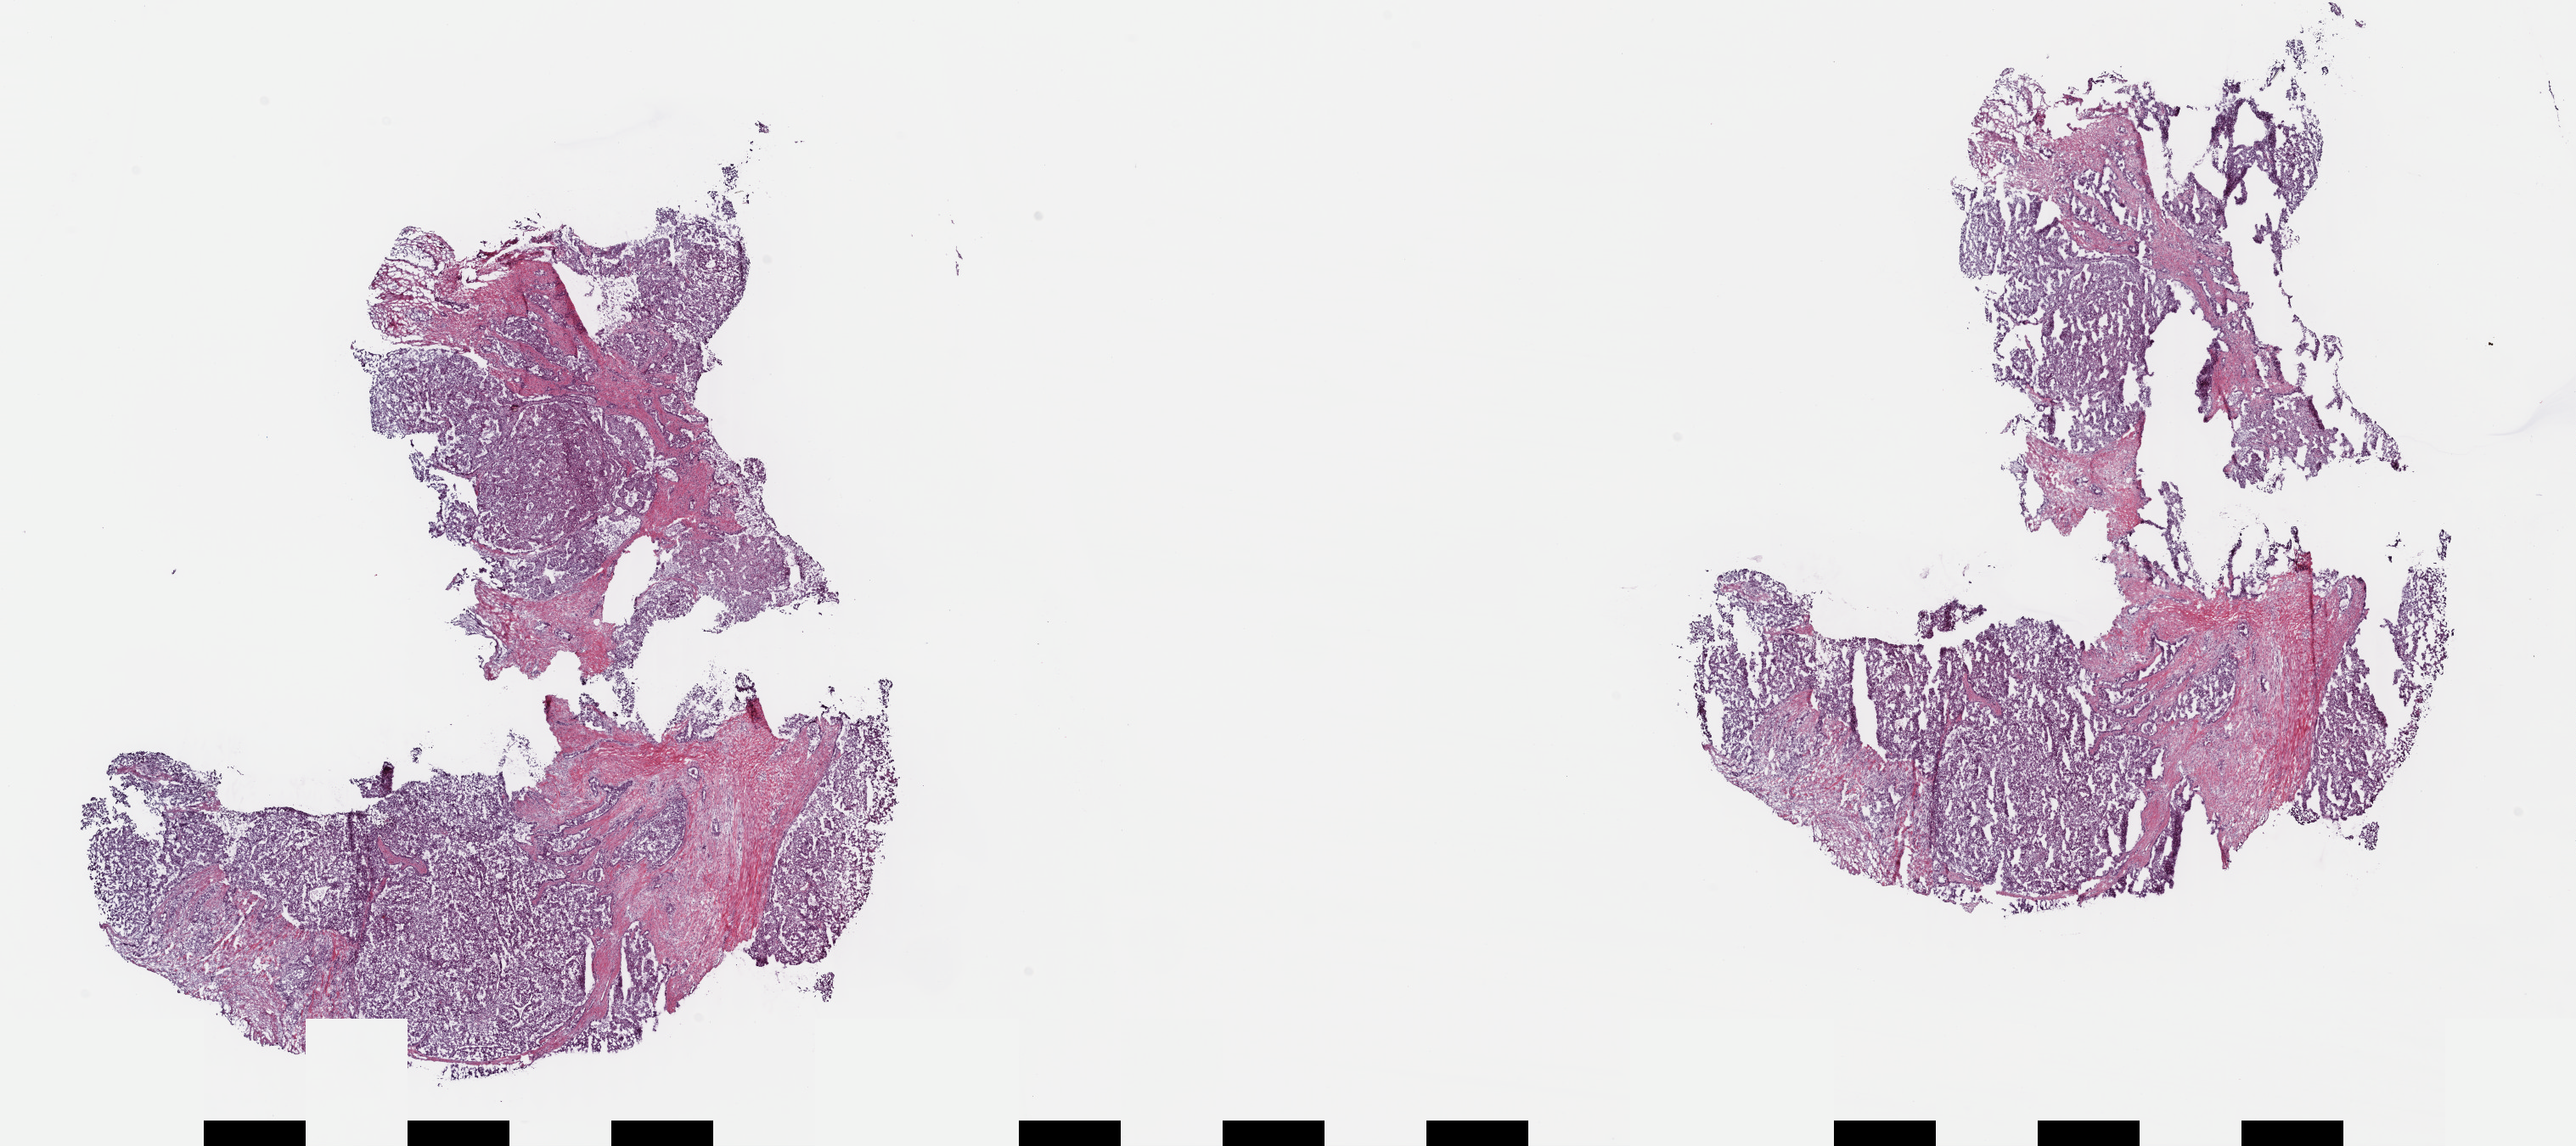
Hematoxylin and eosin (H&E) stained whole-slide image — shown as a low-resolution overview of the whole scanned area (about 23.8 x 10.6 mm, slide scanned at 40x). Frozen section. Kidney, primary tumour sample. Female patient; age at initial diagnosis 61 years. Pathologist review of this section (percent, as recorded): tumour cells 65%, tumour nuclei 85%, normal cells 0%, stromal cells 30%, necrosis 5%. Inflammatory infiltration, as recorded: lymphocyte infiltration 4%, monocyte infiltration 4%, neutrophil infiltration 2%.
* TNM: T3a NX MX
* histologic diagnosis: Papillary adenocarcinoma, NOS
* laterality: right
* AJCC pathologic stage: III (7th edition)